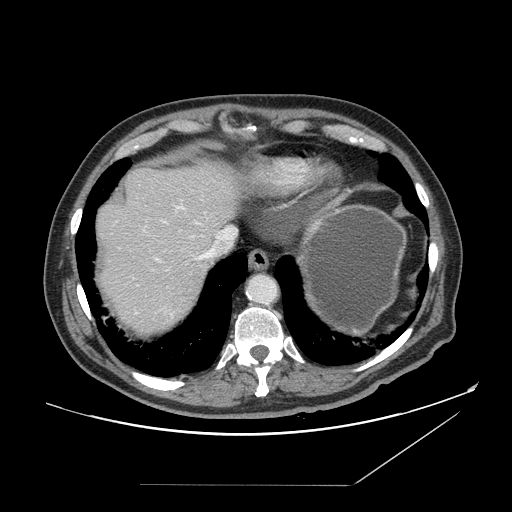
Contrast-enhanced abdominal CT, one axial slice; position 132 of 166 along the scan axis; 120 kVp; intravenous contrast given; soft-tissue window (W 400 / L 40 HU); 2.5 mm slice thickness; 512 × 512 image matrix, field of view 416 × 416 mm. Male patient, age 80 years. From the clinical record (not read from this slice): diagnosis: colorectal cancer liver metastases, imaged before liver resection; multiple liver metastases: no; largest metastasis: 2.2 cm.
Annotated regions visible in this slice (outlined manually by an expert reader):
- hepatic veins: bounding box [x1, y1, x2, y2] px = [154, 221, 236, 262]
- liver: [96, 160, 245, 336]
- planned liver remnant (the part of the liver to remain after resection): [95, 160, 244, 258]
- portal vein (with intrahepatic branches): [177, 207, 184, 210]